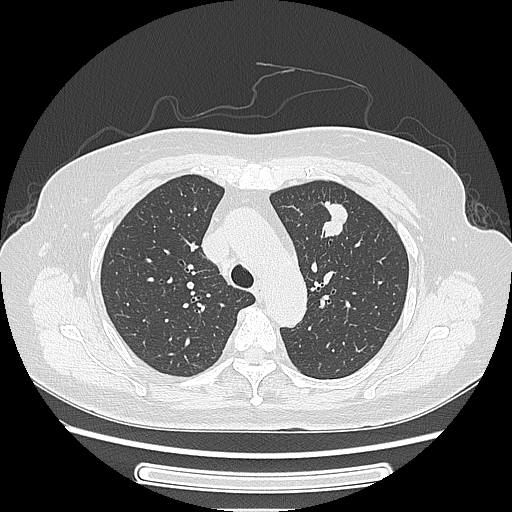
Chest CT, one axial slice; 120 kVp; lung window (W 1500 / L -600 HU); 1.25 mm slice thickness; 512 × 512 image matrix. Female patient, age 77 years. Case-level facts recorded for this patient, not image findings: clinical TNM (as recorded): T1c N3 M0.
Structures marked on this image (rectangle marked by the reading radiologist):
- lung tumour (recorded histology: adenocarcinoma): bounding box <316,190,353,241> (left, top, right, bottom; pixels)